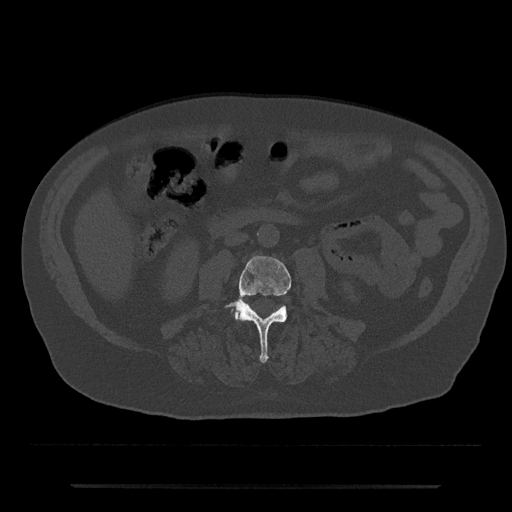
CT including the spine, one axial slice; position 403 of 797 along the scan axis; reconstruction kernel Br40s/3; bone window (W 1800 / L 400 HU); 0.5 mm slice thickness; 512 × 512 image matrix, field of view 434 × 434 mm. Male patient, age 80 years. From the clinical record (not read from this slice): primary cancer: prostate.
Outlined on this slice (semi-automatically segmented with operator editing):
- L3 vertebra: bounding box (x1, y1, x2, y2) in pixels: (226, 256, 292, 363)
- L4 vertebra: (233, 311, 238, 319)